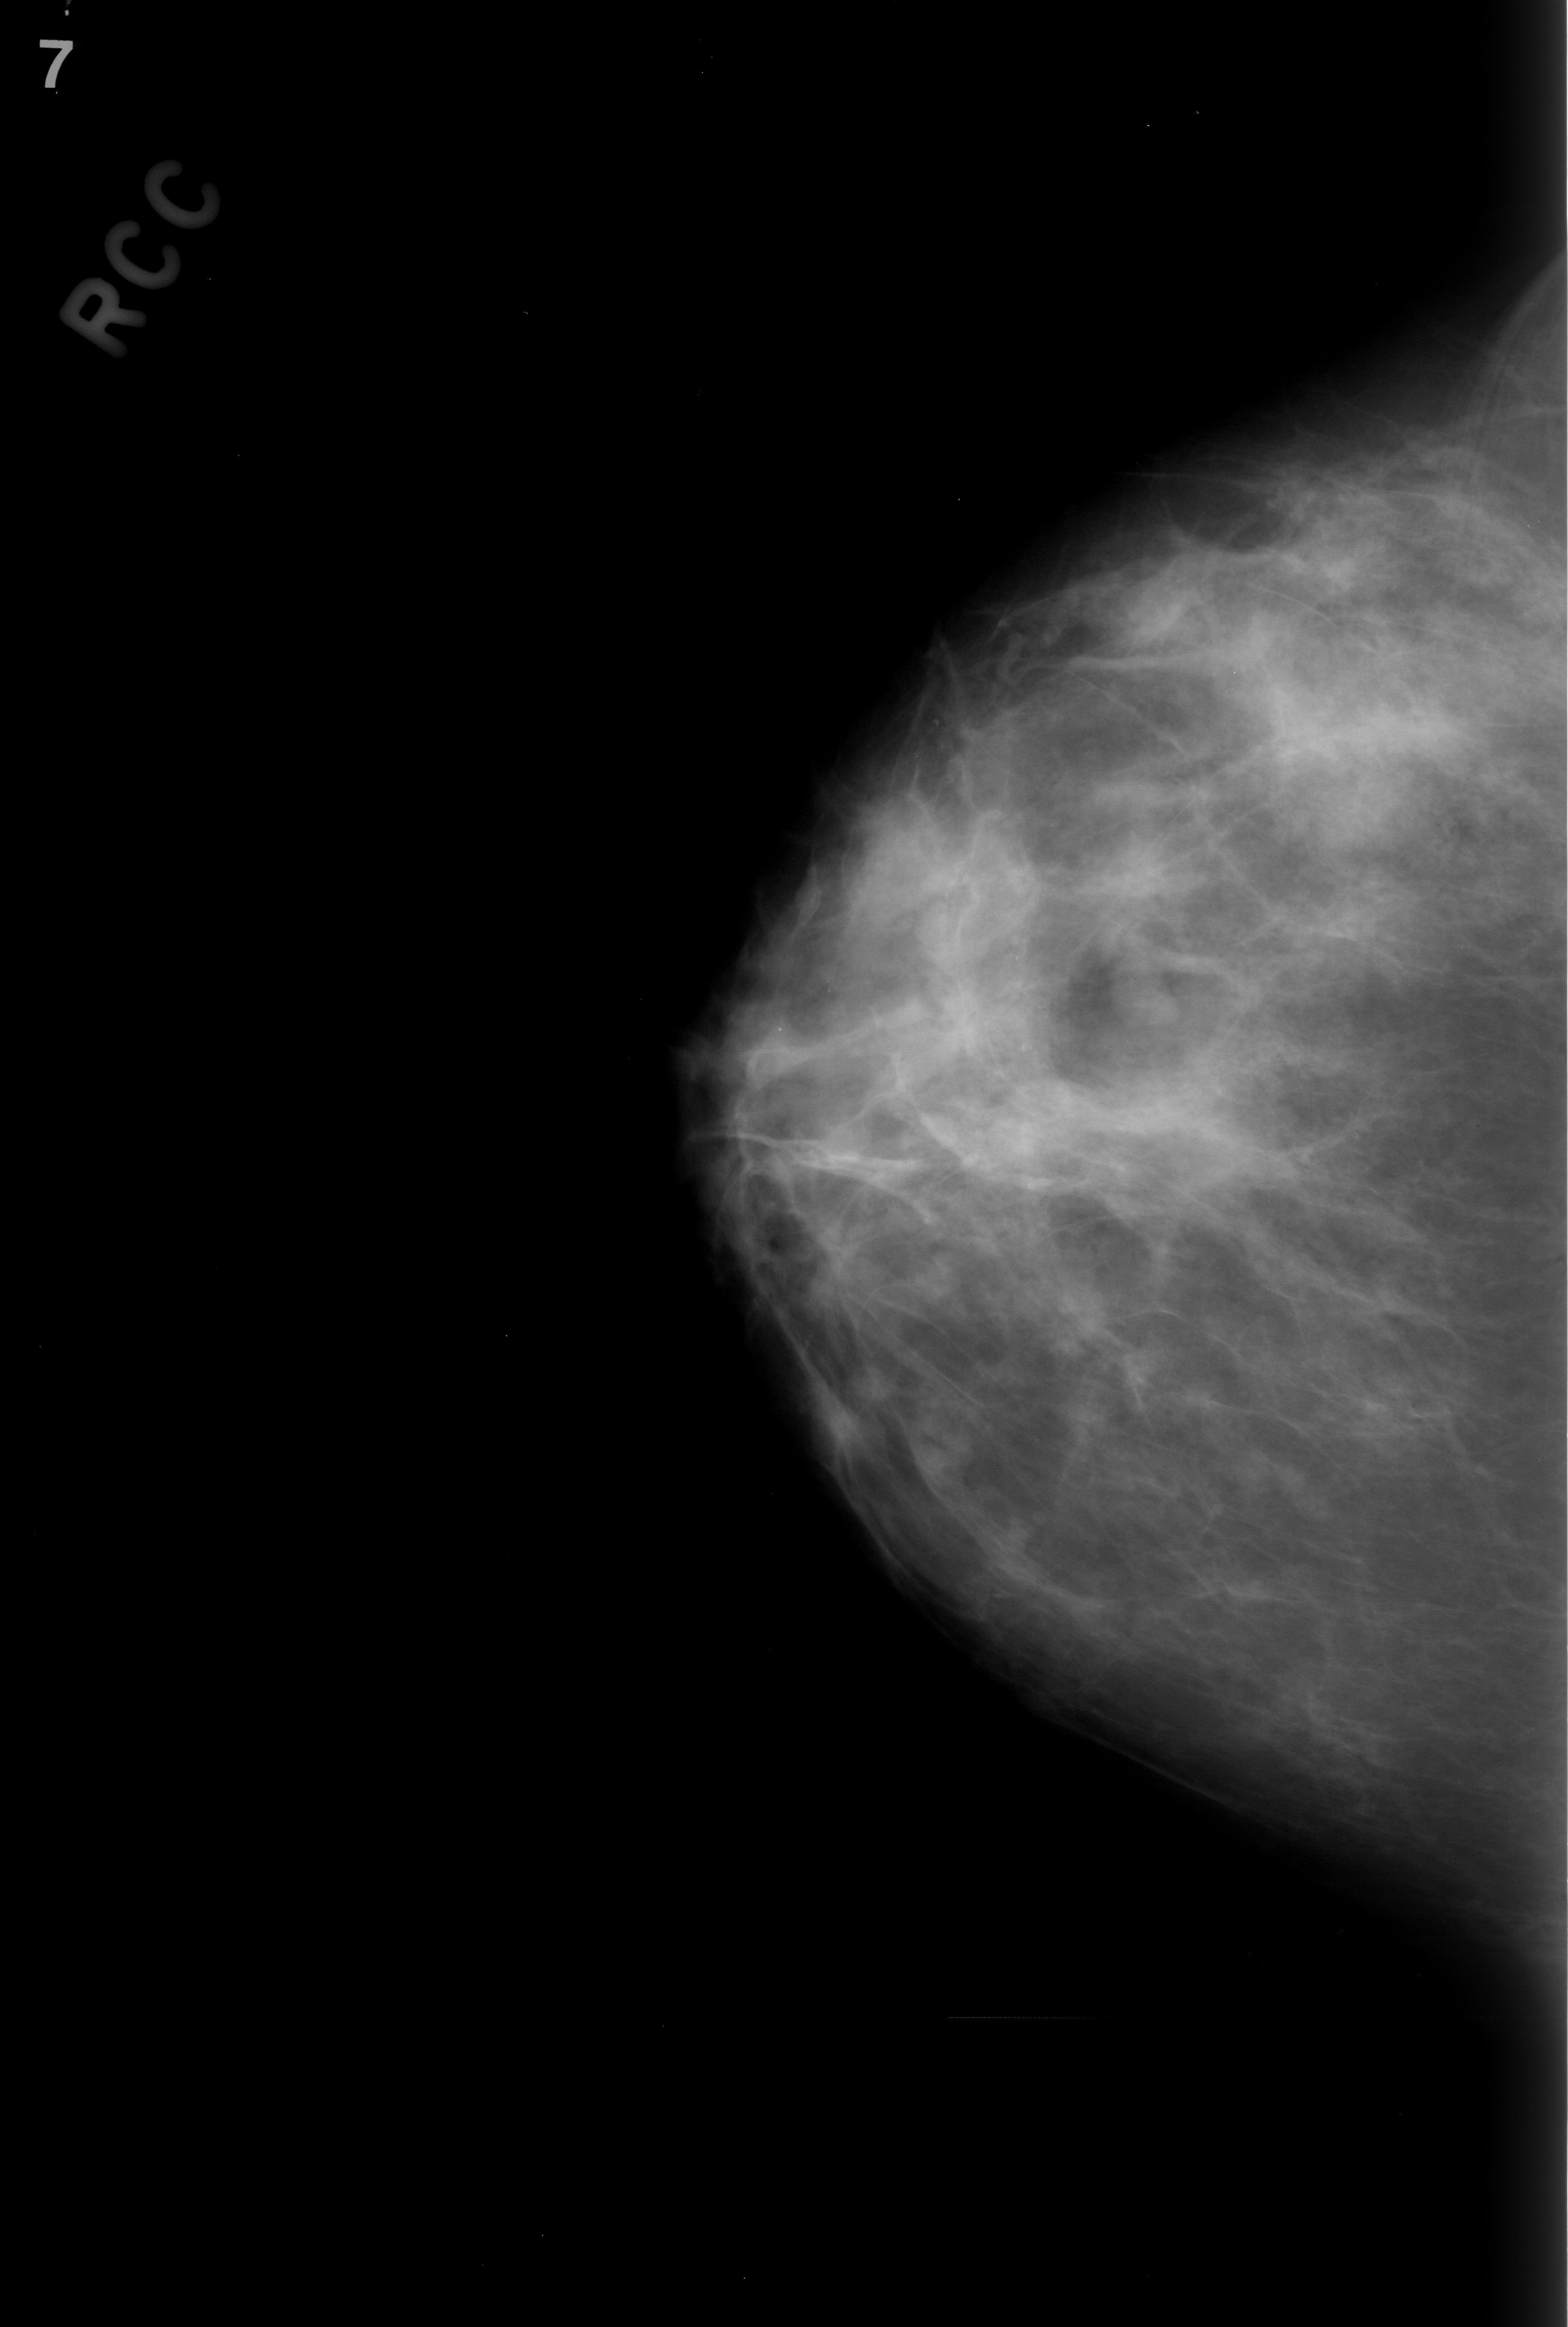
Mammogram (digitized film). Right breast. Craniocaudal (CC) view. BI-RADS breast density category 2 (scale 1–4). 1568 × 2327 image matrix.
Marked abnormalities (boxes around the expert regions of interest):
- mass, shape lobulated, margins circumscribed; BI-RADS assessment category 3; subtlety rating 4 on a 1 (subtle) to 5 (obvious) scale; pathology result (as recorded, not read from the image): benign: box from (x=1111, y=932) to (x=1192, y=1020) px